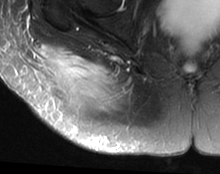
MRI of an extremity soft-tissue mass, one axial slice; position 16 of 63 along the scan axis; T2-weighted fat-saturated; MR volume resampled by the dataset authors to the PET/CT grid (not the native acquisition matrix); 220 × 174 image matrix, field of view 215 × 170 mm. Female patient. From the clinical record (not read from this slice): histological type: spindle cell suggestive of myxofibrosarcoma; grade: intermediate; site of the primary tumour: right buttock.
Annotated regions visible in this slice (expert contour drawn on MRI and transferred to this co-registered scan by the dataset authors):
- gross tumour volume (mass): bounding box [x1, y1, x2, y2] px = [38, 45, 119, 115]